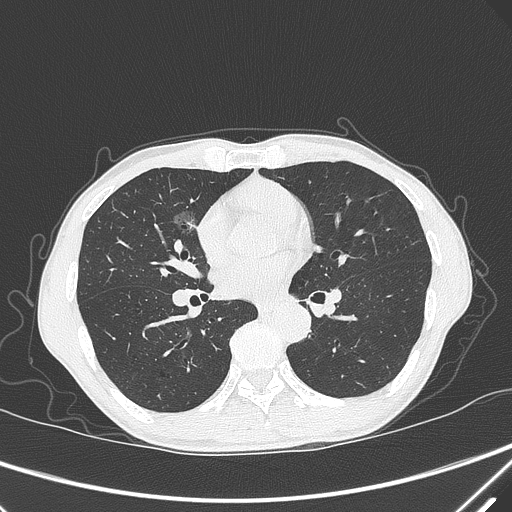
Chest CT, one axial slice; position 166 of 339 along the scan axis; 120 kVp; lung window (W 1500 / L -600 HU); 512 × 512 image matrix, field of view 350 × 350 mm. Patient: male, 67 years. Case-level facts recorded for this patient, not image findings: clinical TNM (as recorded): T1c N0 M0; histopathological grade: G1-2.
Annotated regions visible in this slice (rectangle marked by the reading radiologist):
- lung tumour (recorded histology: adenocarcinoma): bounding box [x1, y1, x2, y2] px = [172, 207, 203, 242]